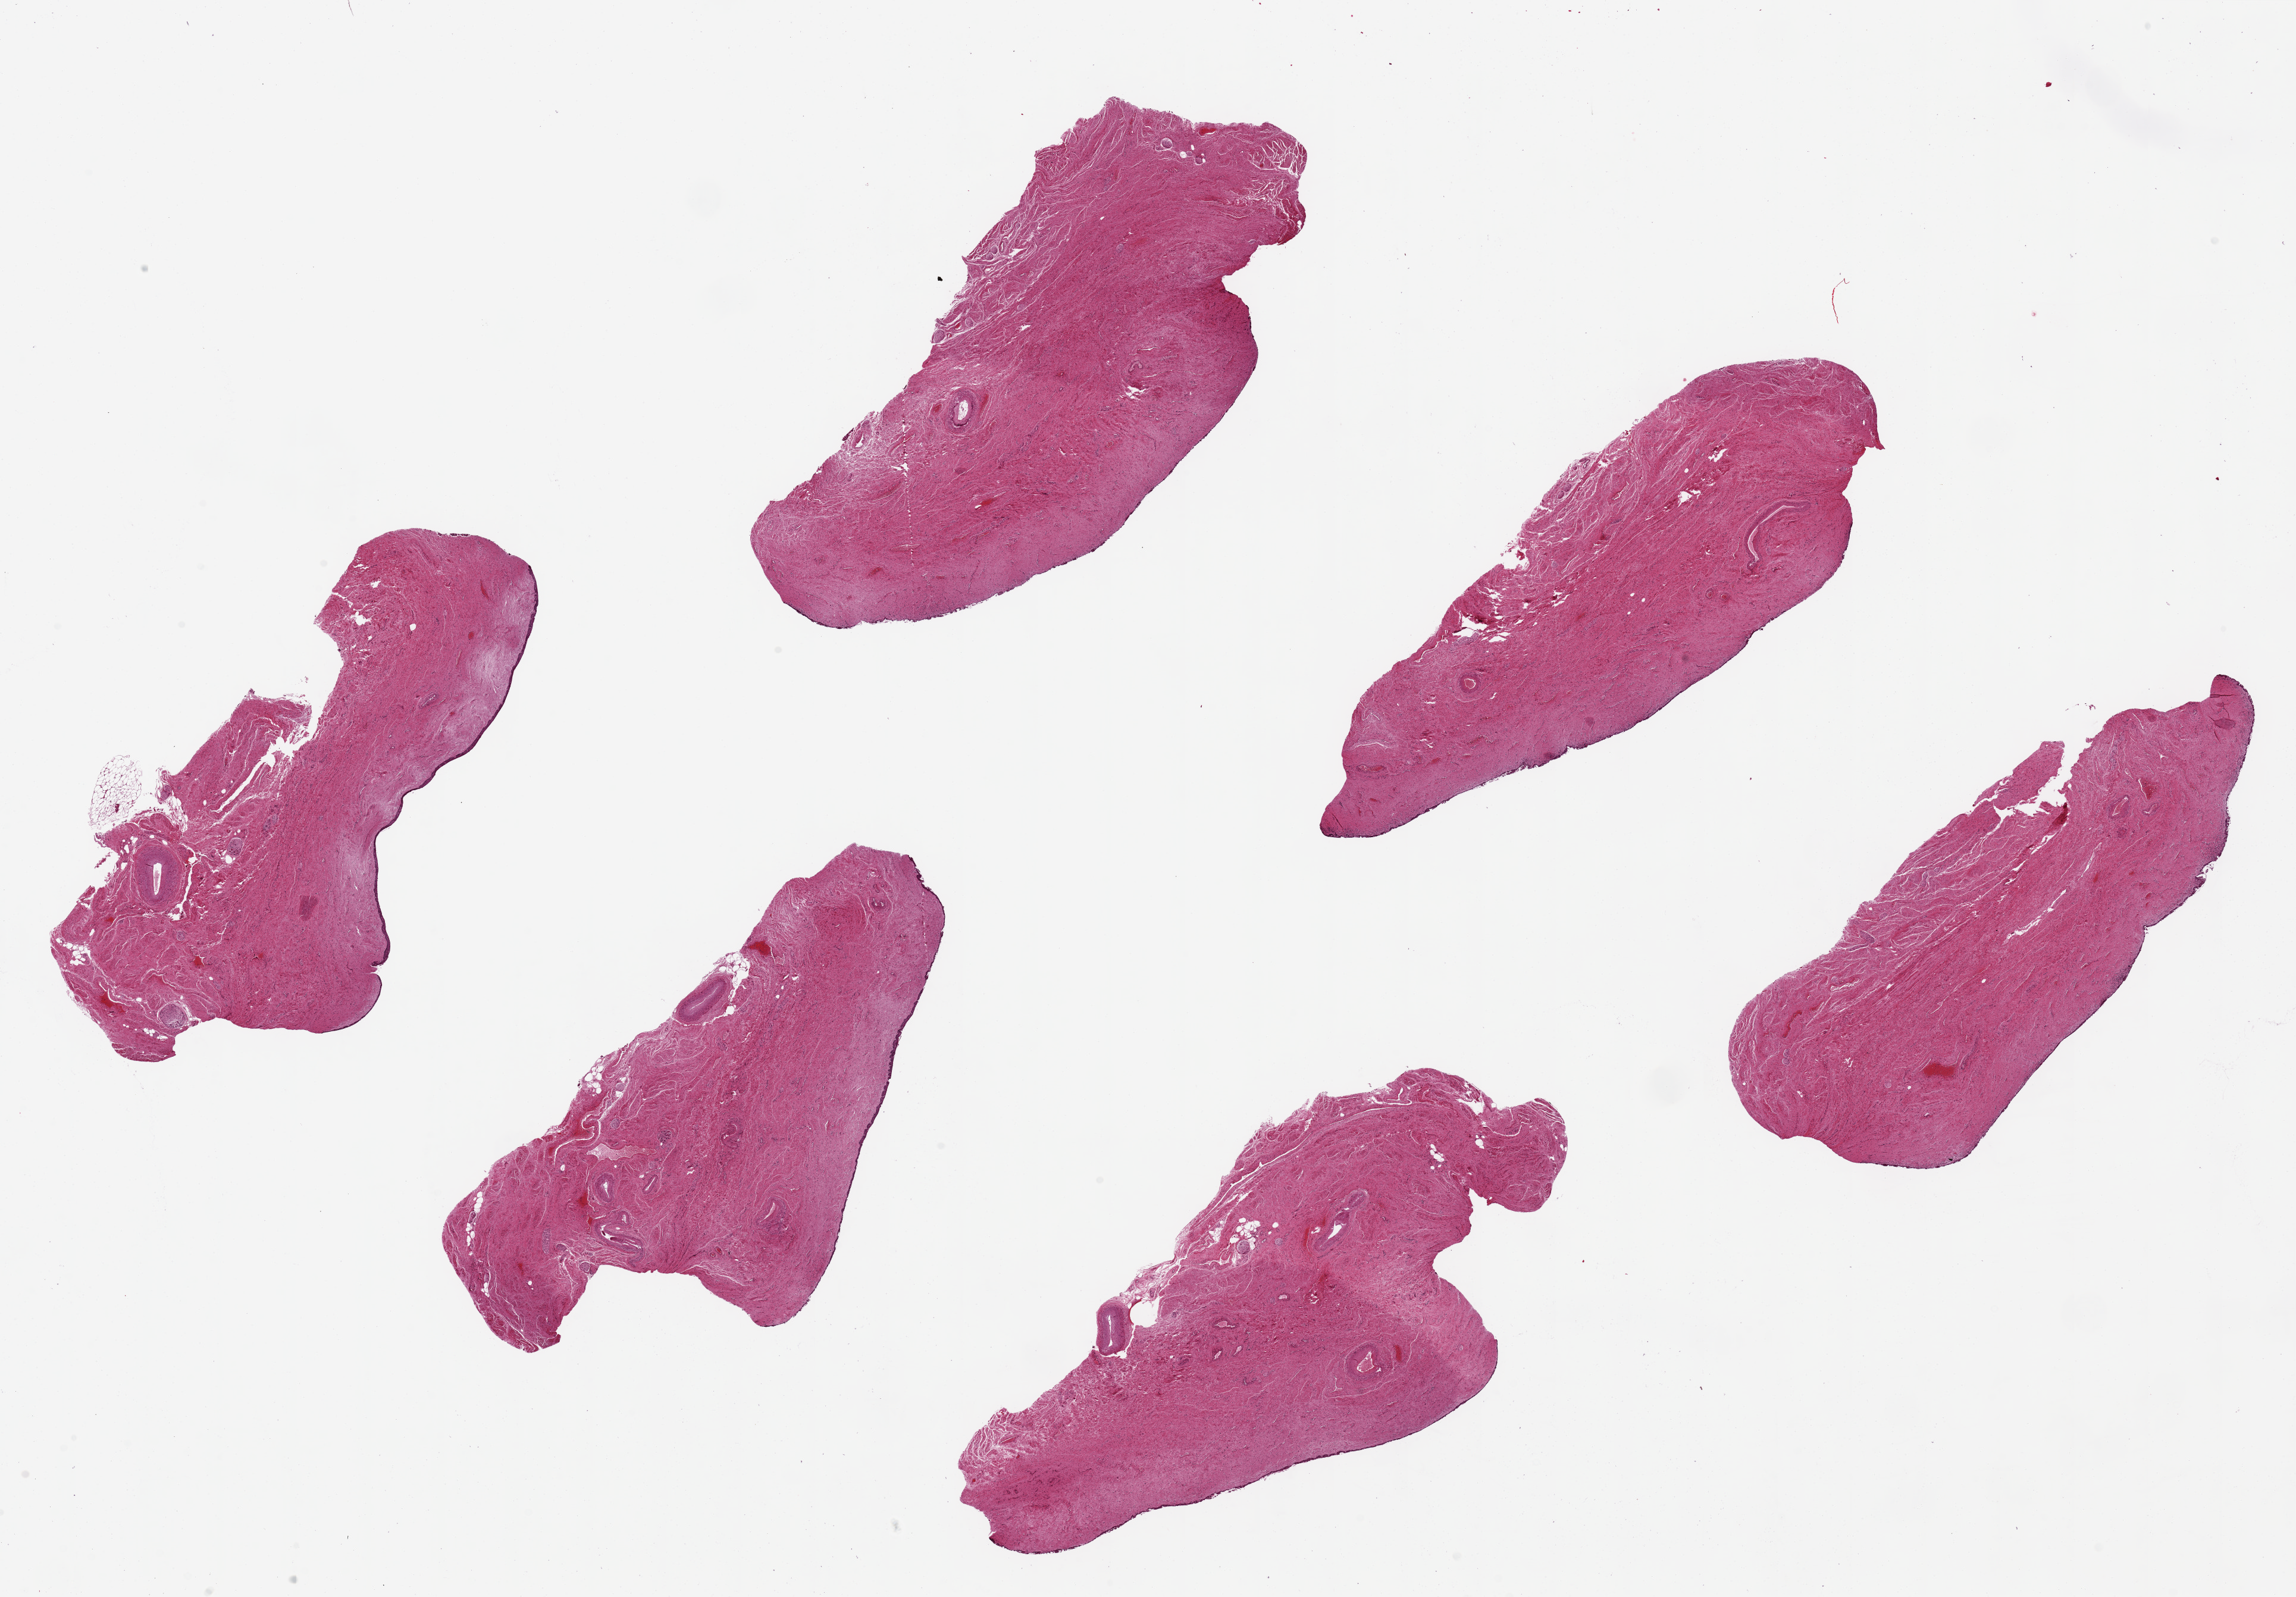
Whole-slide image, H&E stain, low-resolution overview of the scanned area, about 30.5 x 21.2 mm, PAXgene-fixed paraffin-embedded (PFPE) section, sampled site (target tissue): vagina, tissue donor sample. Donor sex: female.
Review note (as recorded): 6 pieces ~8.5x3mm; squamous mucosa is <1% of thickness.